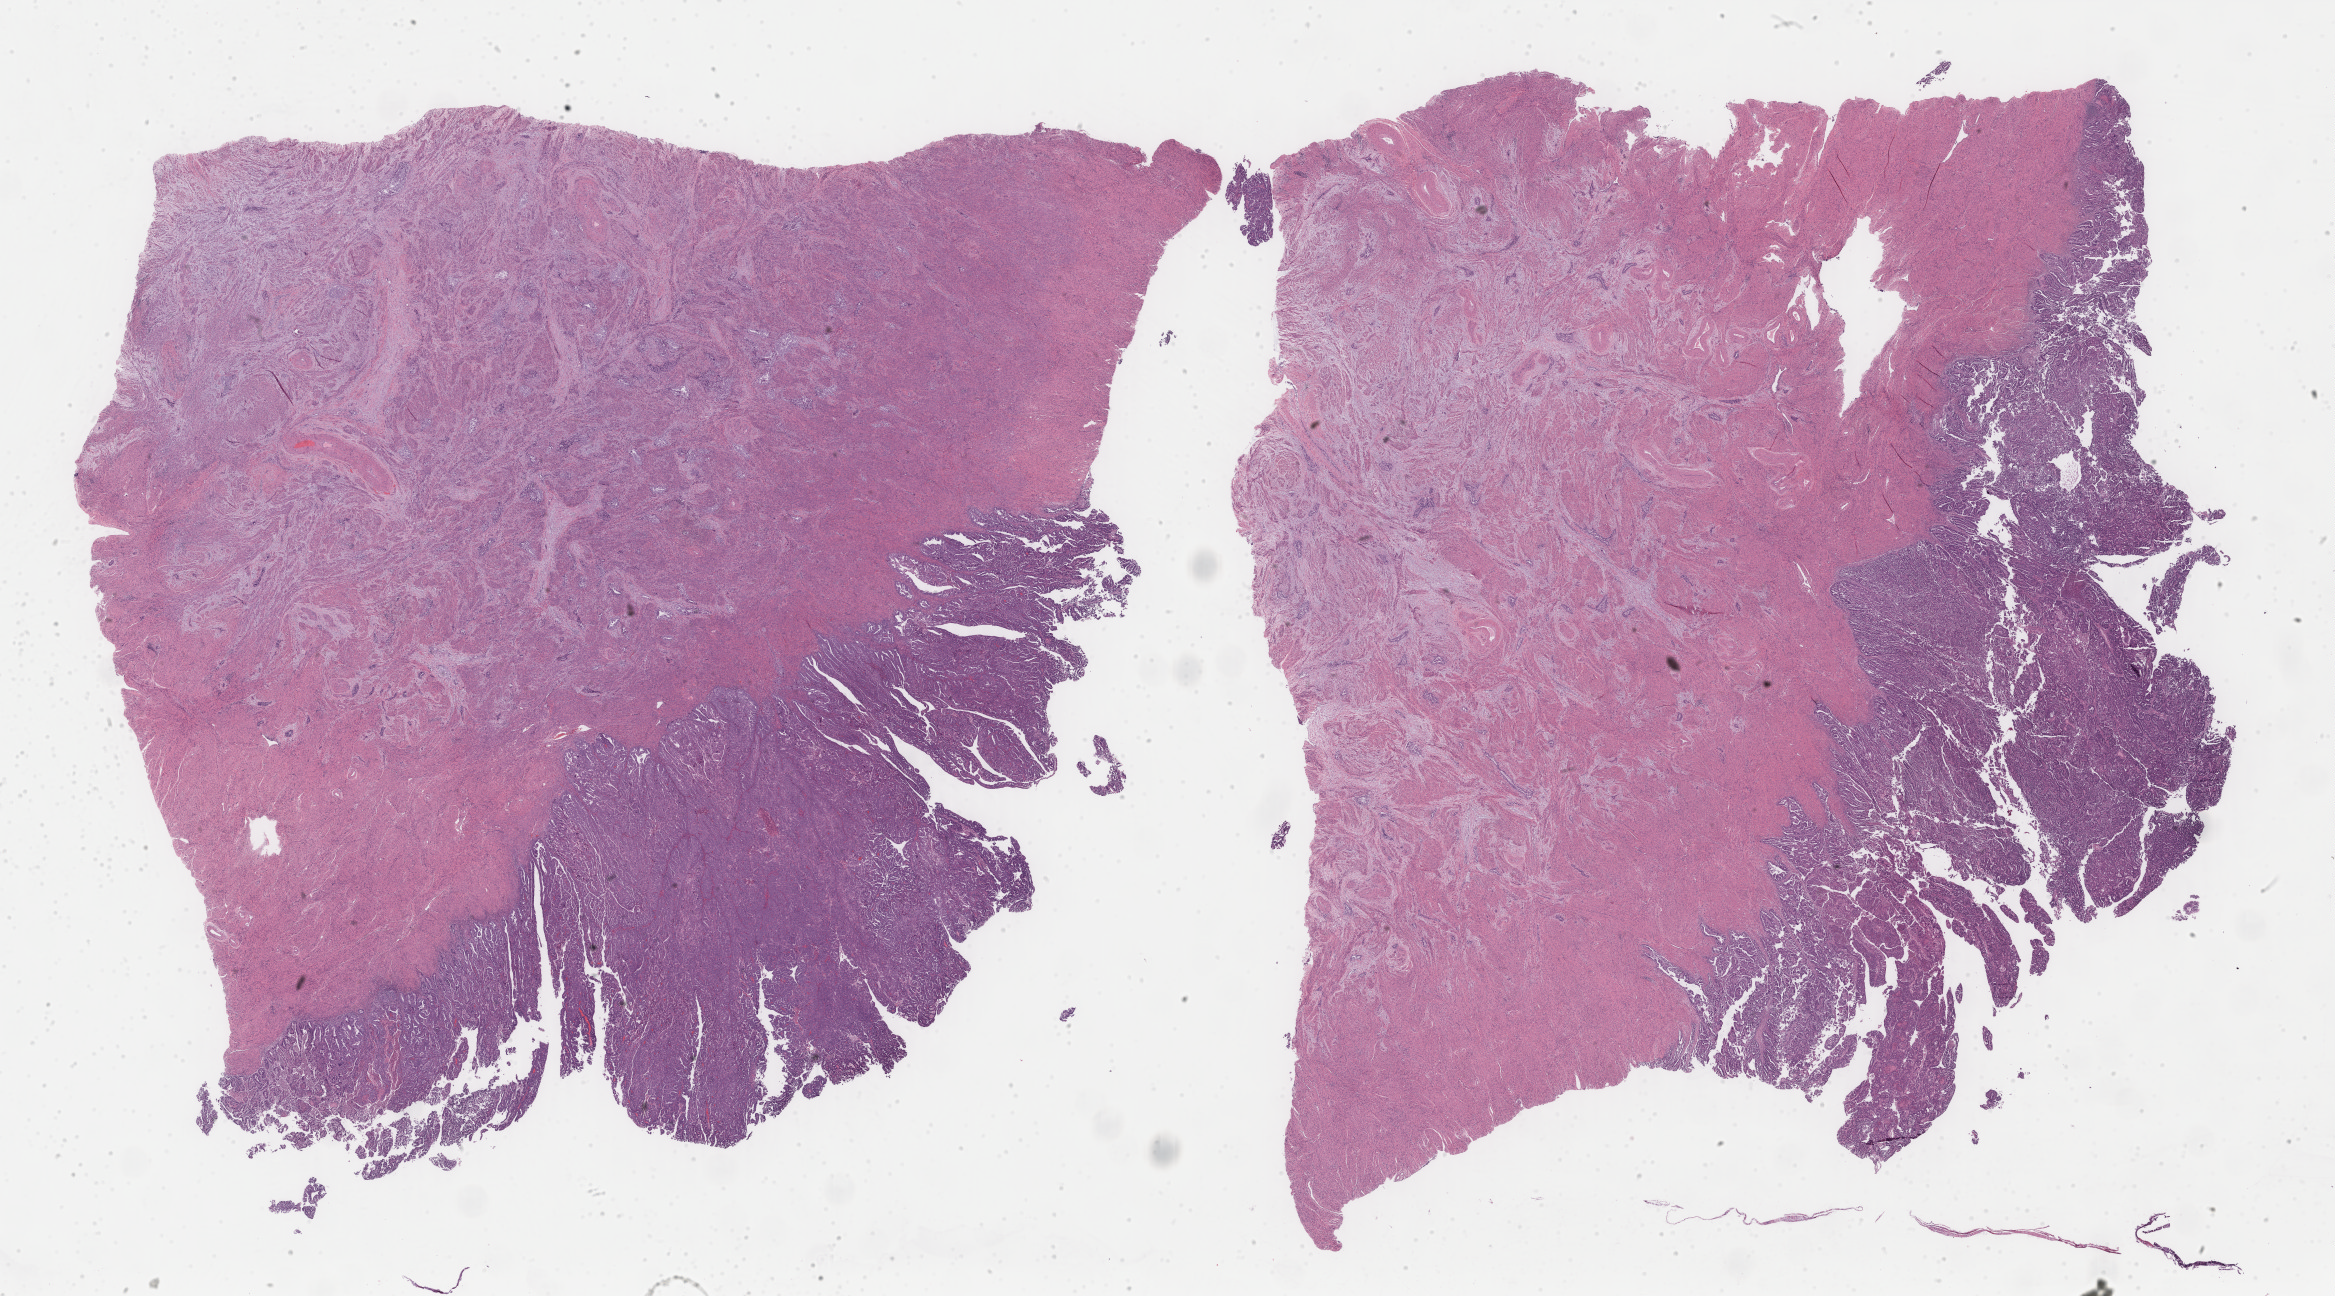
Digitized Hematoxylin and eosin (H&E) stained tissue section (whole slide), whole scanned area (about 37.1 x 20.6 mm, from a 40x scan) shown as a low-resolution overview; formalin-fixed paraffin-embedded (FFPE) diagnostic section; sample: primary tumour, uterus. Female, age 66 years at initial diagnosis. Histologic grade: G3 (poorly differentiated).
Diagnosis: Serous cystadenocarcinoma, NOS (endometrium). FIGO stage: IIIC.